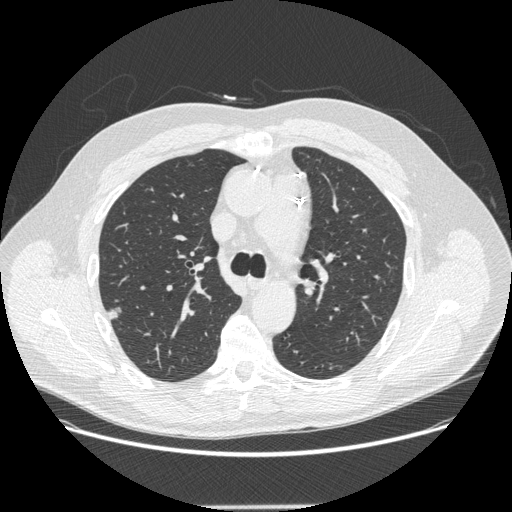
Low-dose screening chest CT, axial slice, third screening round (two years after baseline), lung window (W 1500 / L -600 HU), 1.25 mm slice thickness. Male participant, aged 62 years at enrolment. Current smoker at enrolment.
• Lesion marked by an expert reader, bounding box (x1, y1, x2, y2) in pixels: (94, 298, 133, 336).
• Screening reader's record for this exam (one nodule recorded; not confirmed to be the boxed lesion): non-calcified nodule or mass ≥4 mm, right upper lobe, 12 × 11 mm, smooth margins, soft tissue attenuation, pre-existing on the prior screen: yes; interval growth: yes.
• Official screen result: positive, other.
• Later outcome: lung cancer diagnosed 112 days after this screen — adenocarcinoma, NOS, right upper lobe, moderately differentiated (G2), stage IA (AJCC 6th edition), 12 mm at pathology.